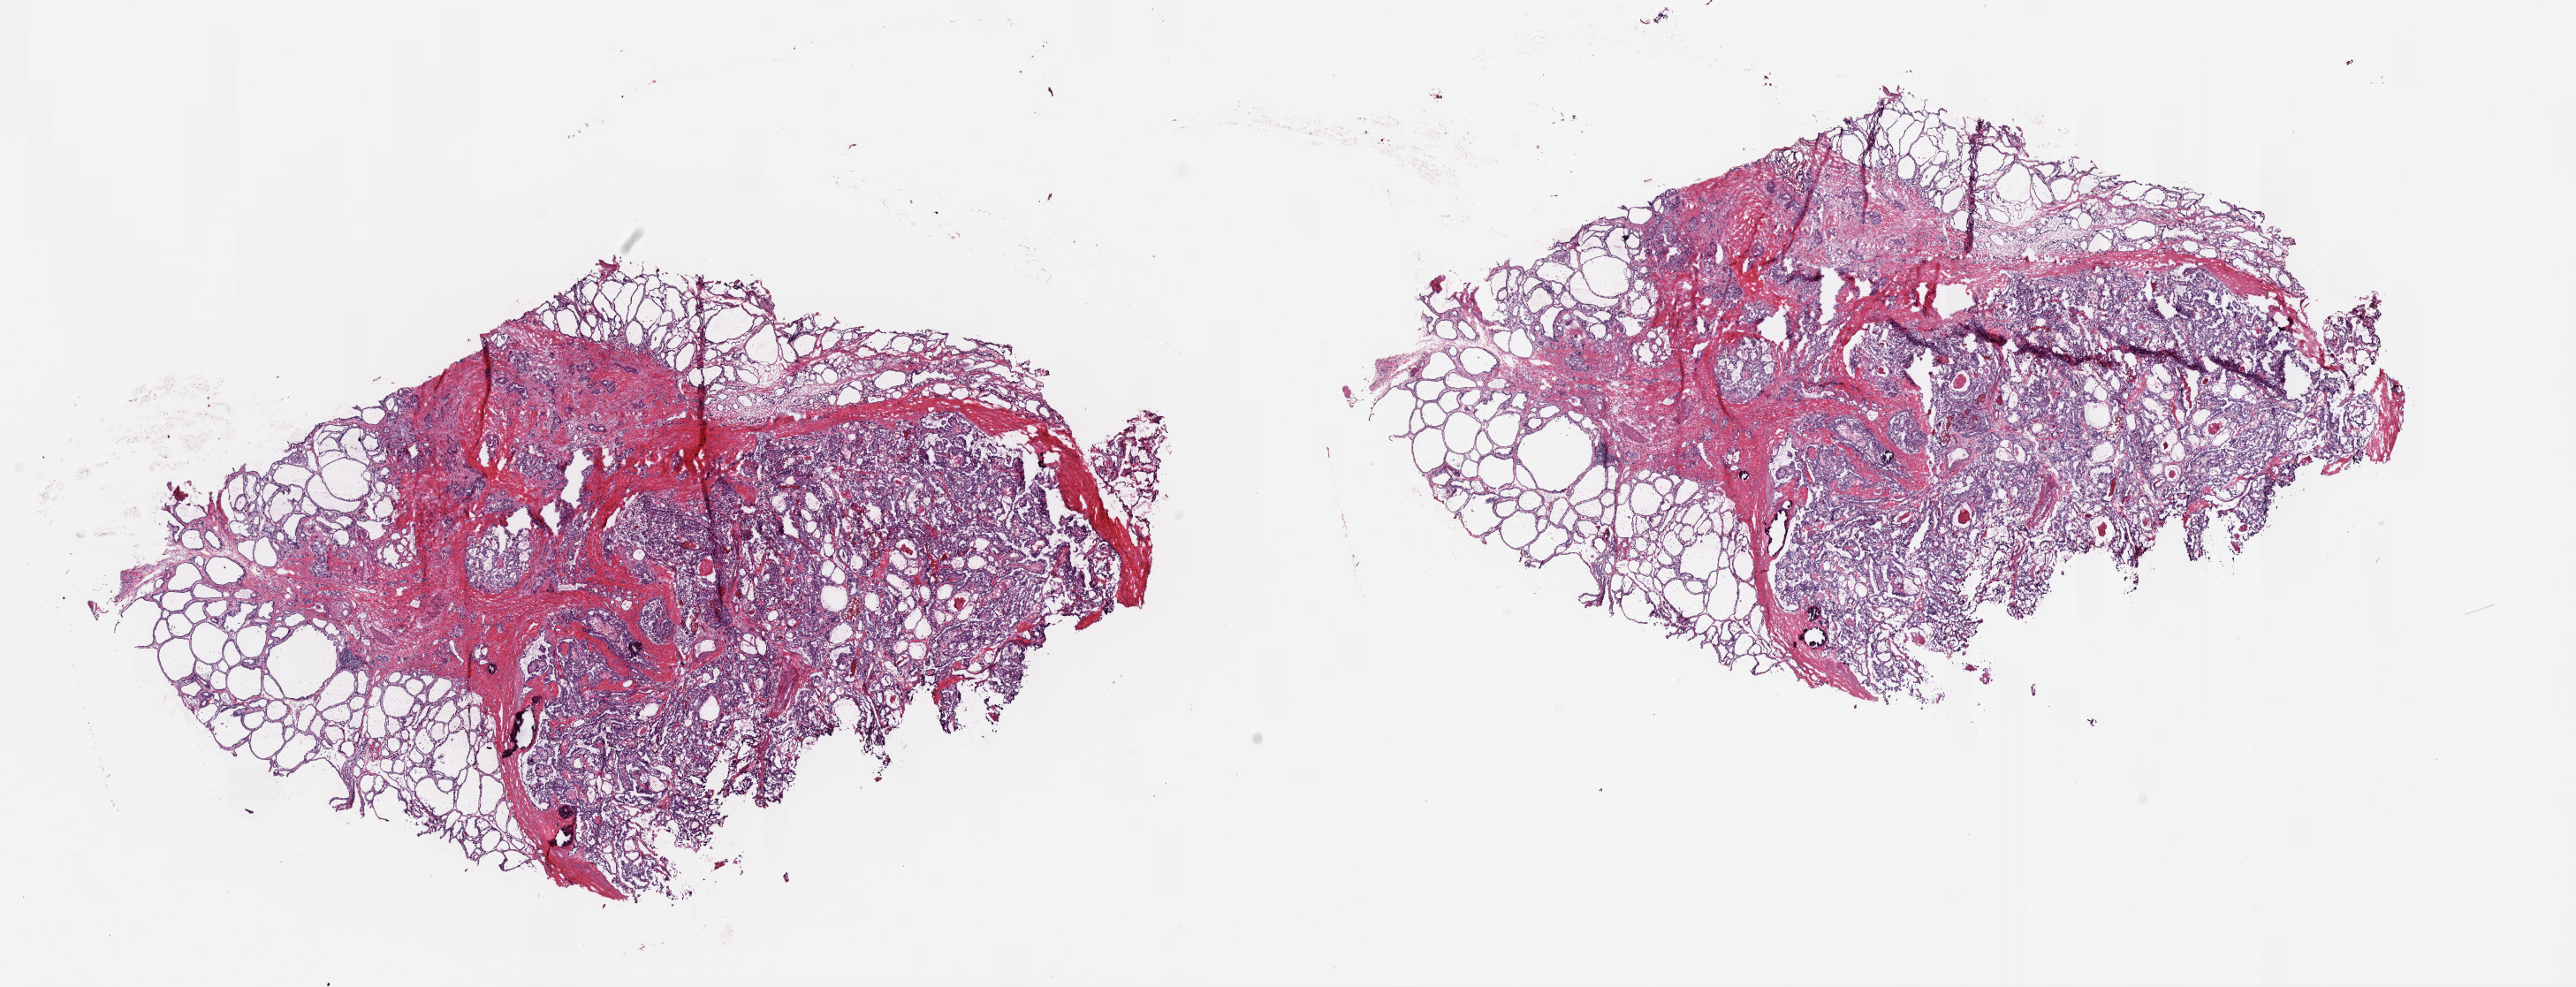
Whole-slide histology image, H&E-stained, shown as a low-resolution overview of the whole scanned area (about 23.0 x 8.8 mm); frozen section from the top of the tissue portion; thyroid, primary tumour sample. Female patient; age at initial diagnosis 27 years. Composition of this section per pathologist review: tumour cells 50%, tumour nuclei 80%, normal cells 20%, stromal cells 30%, necrosis 0%. Inflammatory infiltration, as recorded: lymphocyte infiltration 0%, monocyte infiltration 1%, neutrophil infiltration 0%.
AJCC pathologic stage: I. Pathologic diagnosis: Papillary adenocarcinoma, NOS (thyroid gland). TNM: T1 N0 MX. Lymph nodes positive (case pathology): 0 of 2 examined.